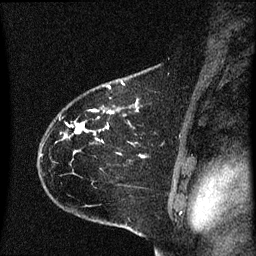
Breast MRI (dynamic contrast-enhanced), one sagittal slice; slice 47 of 60 in the series (ordered by position); dynamic contrast-enhanced series, image 2 of 3 at this slice position (ordered by acquisition); 1.5 T; TE 4.2 ms, TR 8.4 ms; 2 mm slice thickness; 256 × 256 image matrix, field of view 200 × 200 mm. Patient: female, 35 years. From the clinical record (not read from this slice): setting: breast cancer imaged before/during neoadjuvant chemotherapy; receptor status: HER2-positive.
Structures marked on this image (semi-automatically segmented with operator editing):
- analysis volume of interest (the breast-tissue region the enhancement analysis was run in; not a lesion): bounding box [x1, y1, x2, y2] px = [40, 68, 169, 173]
- tumour enhancement mask (voxels above the 70 % enhancement threshold inside the analysis volume of interest): [75, 82, 123, 133]